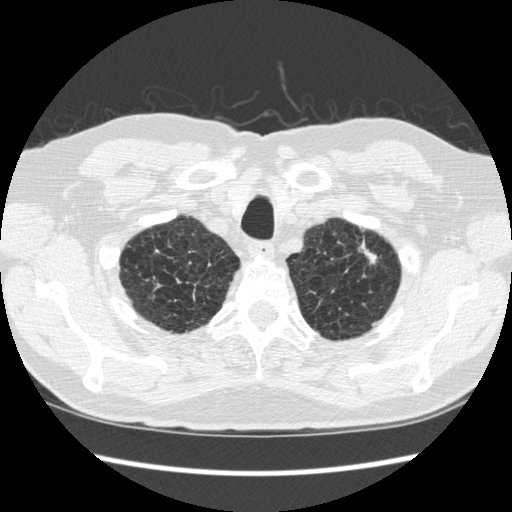
Axial slice from a low-dose chest CT screening exam; second screening round (one year after baseline); lung window (W 1500 / L -600 HU); 1.25 mm slice thickness; 120 kVp. Male participant, aged 70 years at enrolment.
- Expert reader's lesion annotation, bounding box (x1, y1, x2, y2) in pixels: (326, 229, 388, 298).
- The screening reader recorded 5 non-calcified nodules or masses ≥4 mm on this exam (right lower lobe, right lower lobe, right lower lobe, left upper lobe, left lower lobe); which of them this box marks is not recorded.
- Official screen result: positive, change unspecified: nodule(s) >= 4 mm or enlarging nodule(s), mass(es), or other non-specific abnormalities suspicious for lung cancer.
- Later outcome: lung cancer diagnosed 479 days after this screen — squamous cell carcinoma, NOS, left upper lobe, moderately differentiated (G2), stage IA (AJCC 6th edition), 18 mm at pathology.